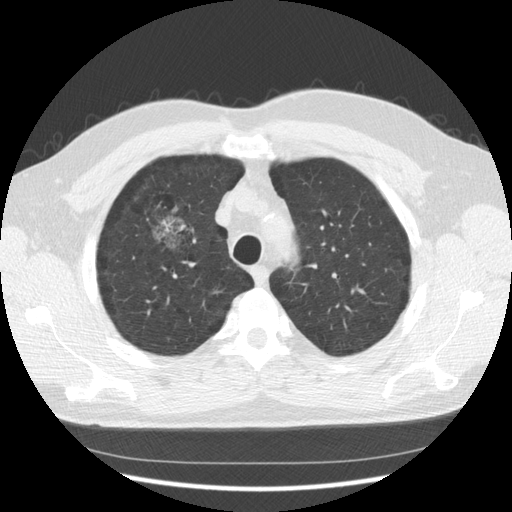
Low-dose screening chest CT, one axial slice; reconstruction kernel STANDARD; lung window (W 1500 / L -600 HU); 2.5 mm slice thickness; 512 × 512 image matrix.
Outlined on this slice (outlined manually by an expert reader):
- lesion 1 (tumor, upper lobe of right lung): bounding box (x1, y1, x2, y2) in pixels: (153, 216, 186, 249)